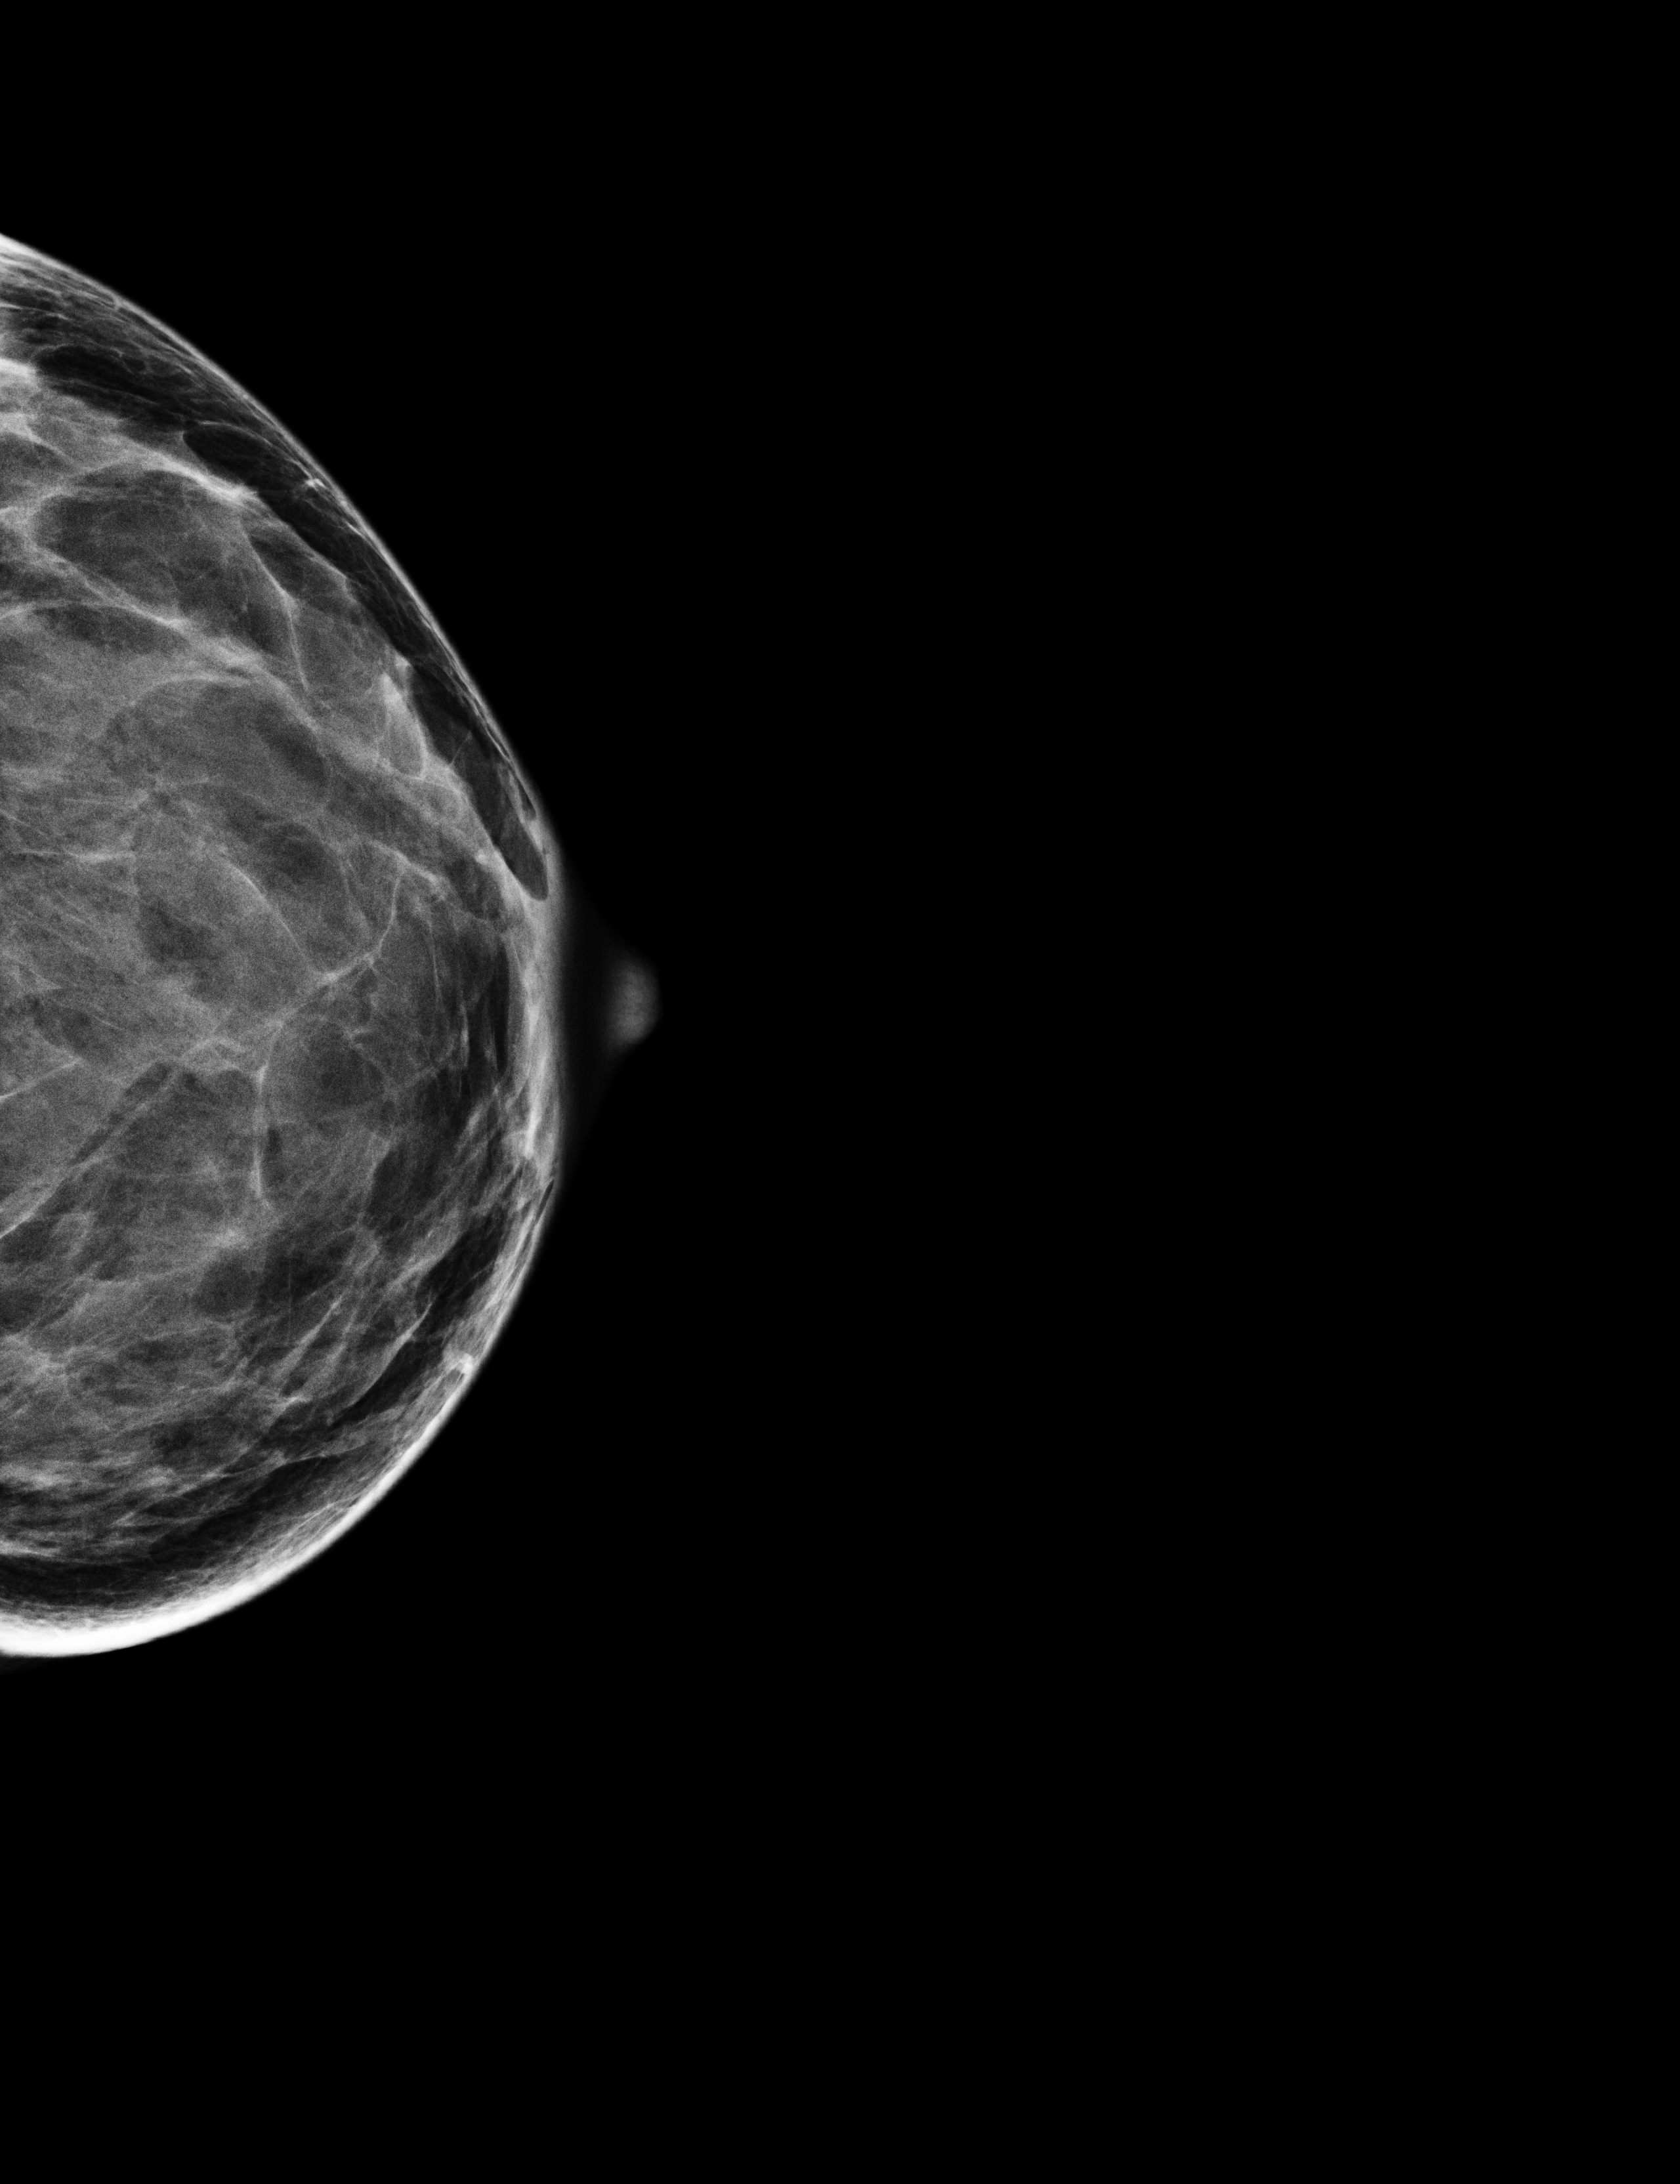
Annual screening mammography examination. Female patient, age 42 years.
Image type: full-field digital mammogram. Breast: left. Projection: craniocaudal (CC) view.